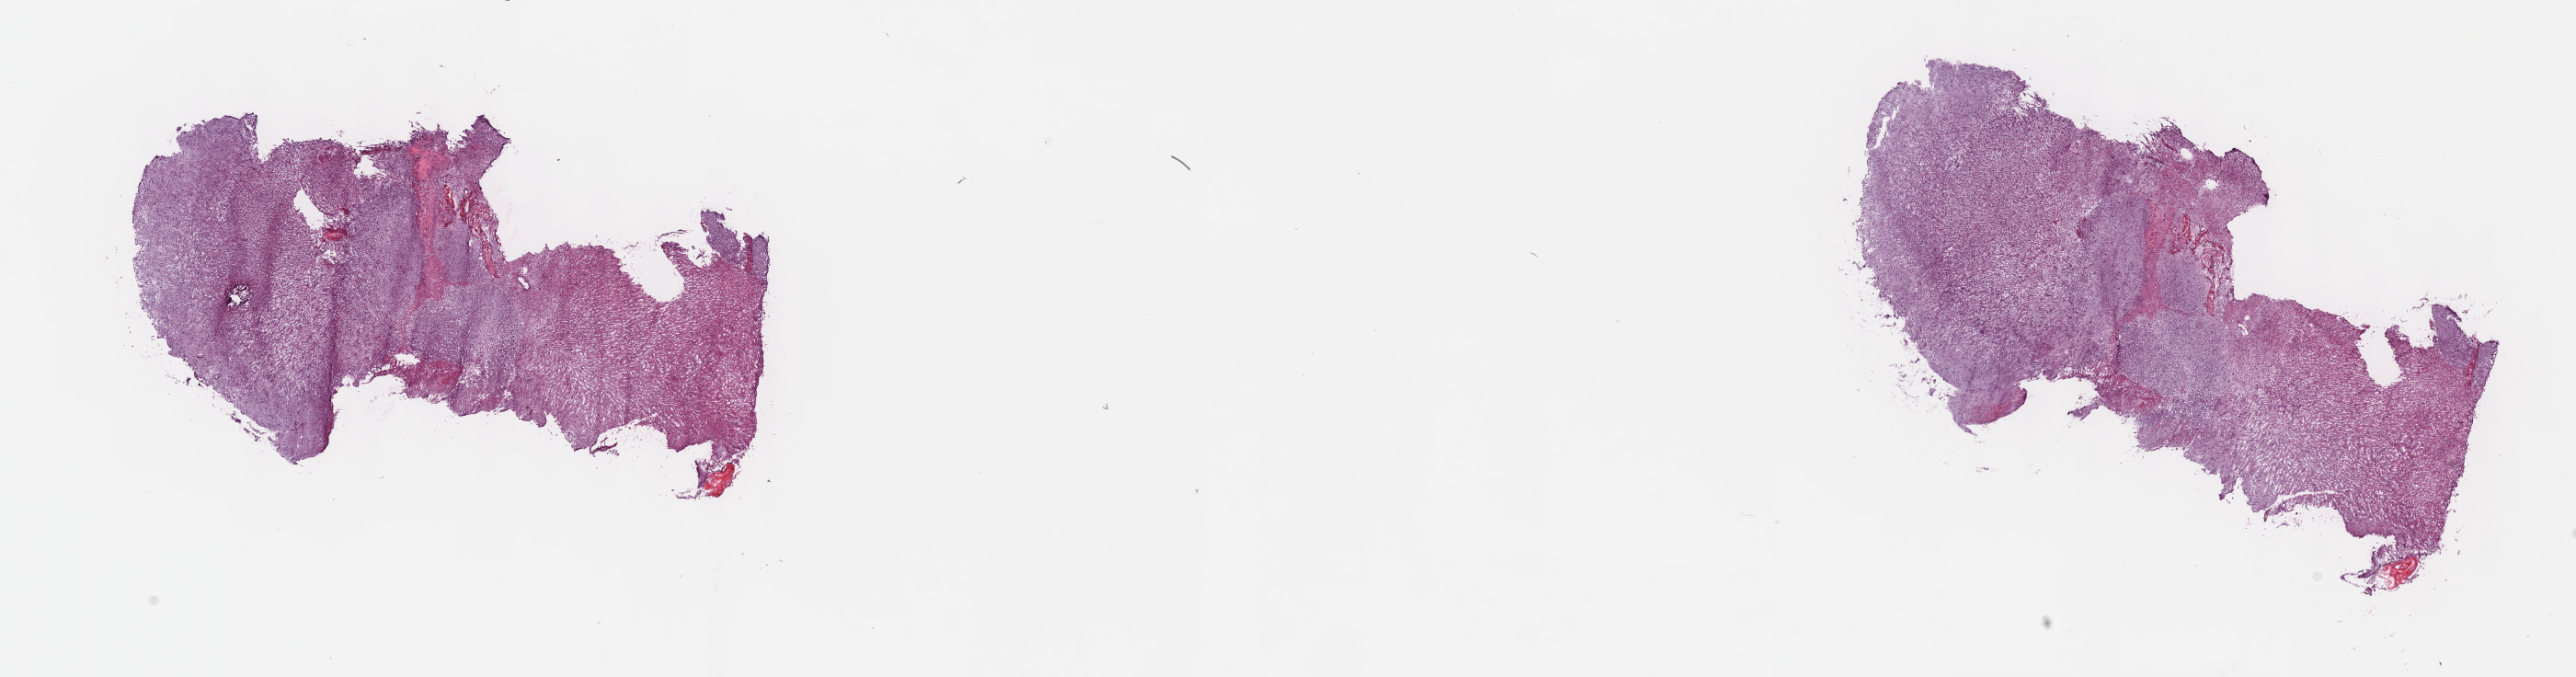
Digitized H&E tissue section (whole slide), low-resolution overview of the scanned area, about 22.7 x 6.0 mm. Frozen section from the top of the tissue portion. Sample: primary tumour, brain. Patient: female, age at initial diagnosis 52 years. Histologic grade: G3 (poorly differentiated). Slide review estimates, as recorded: tumour cells 40%, tumour nuclei 70%, normal cells 10%, stromal cells 50%, necrosis 0%. Infiltration values recorded for this section: lymphocyte infiltration 0%, monocyte infiltration 0%, neutrophil infiltration 0%.
Pathologic diagnosis: Oligodendroglioma, anaplastic (cerebrum). Laterality: left.